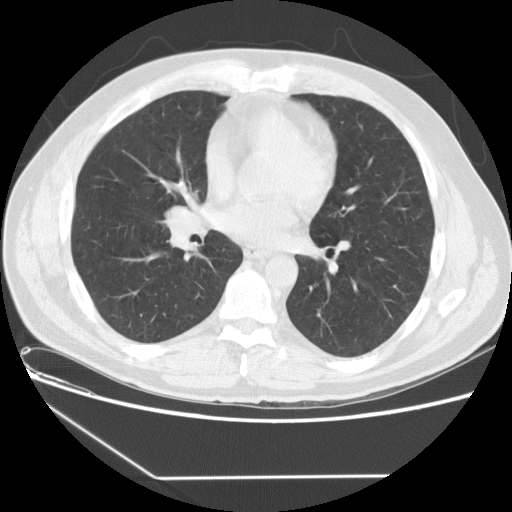
Low-dose screening chest CT, one axial slice. Slice 70 of 154 in the series (ordered by position). Reconstruction kernel STANDARD. 120 kVp. Lung window (W 1500 / L -600 HU). 2.5 mm slice thickness. 512 × 512 image matrix, field of view 370 × 370 mm.
Outlined on this slice (outlined manually by an expert reader):
- lesion 1 (tumor, middle lobe of right lung): bounding box <168,205,197,233> (left, top, right, bottom; pixels)